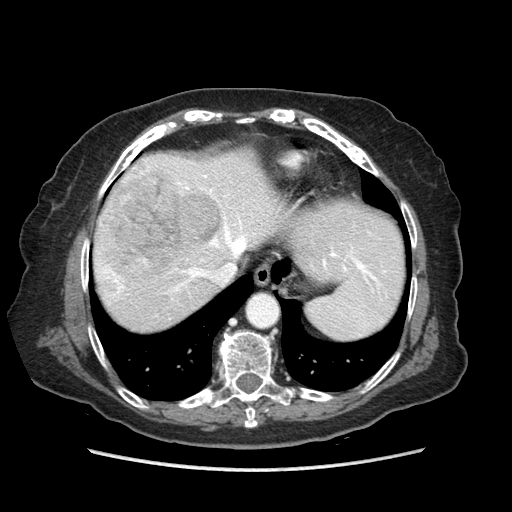
Contrast-enhanced abdominal CT (liver protocol), one axial slice; slice 69 of 89 in the series (ordered by position); reconstruction kernel STANDARD; soft-tissue window (W 400 / L 40 HU); 2.5 mm slice thickness; 512 × 512 image matrix. From the clinical record (not read from this slice): diagnosis: hepatocellular carcinoma (patient treated with transarterial chemoembolisation; whether this scan precedes or follows treatment is not stated here); TNM stage (as recorded): Stage-IIIA; Child-Pugh class: A; tumour nodularity: multinodular; tumour size: 11 cm.
Outlined on this slice (semi-automatic segmentation, software-assisted and operator-edited):
- abdominal aorta: bounding box (x1, y1, x2, y2) in pixels: (248, 295, 277, 326)
- liver parenchyma outside the tumour (the mass and vessels are separate outlines, so this box may not span the whole liver): (92, 152, 402, 330)
- mass: (97, 167, 219, 281)
- liver vessels: (101, 175, 367, 293)